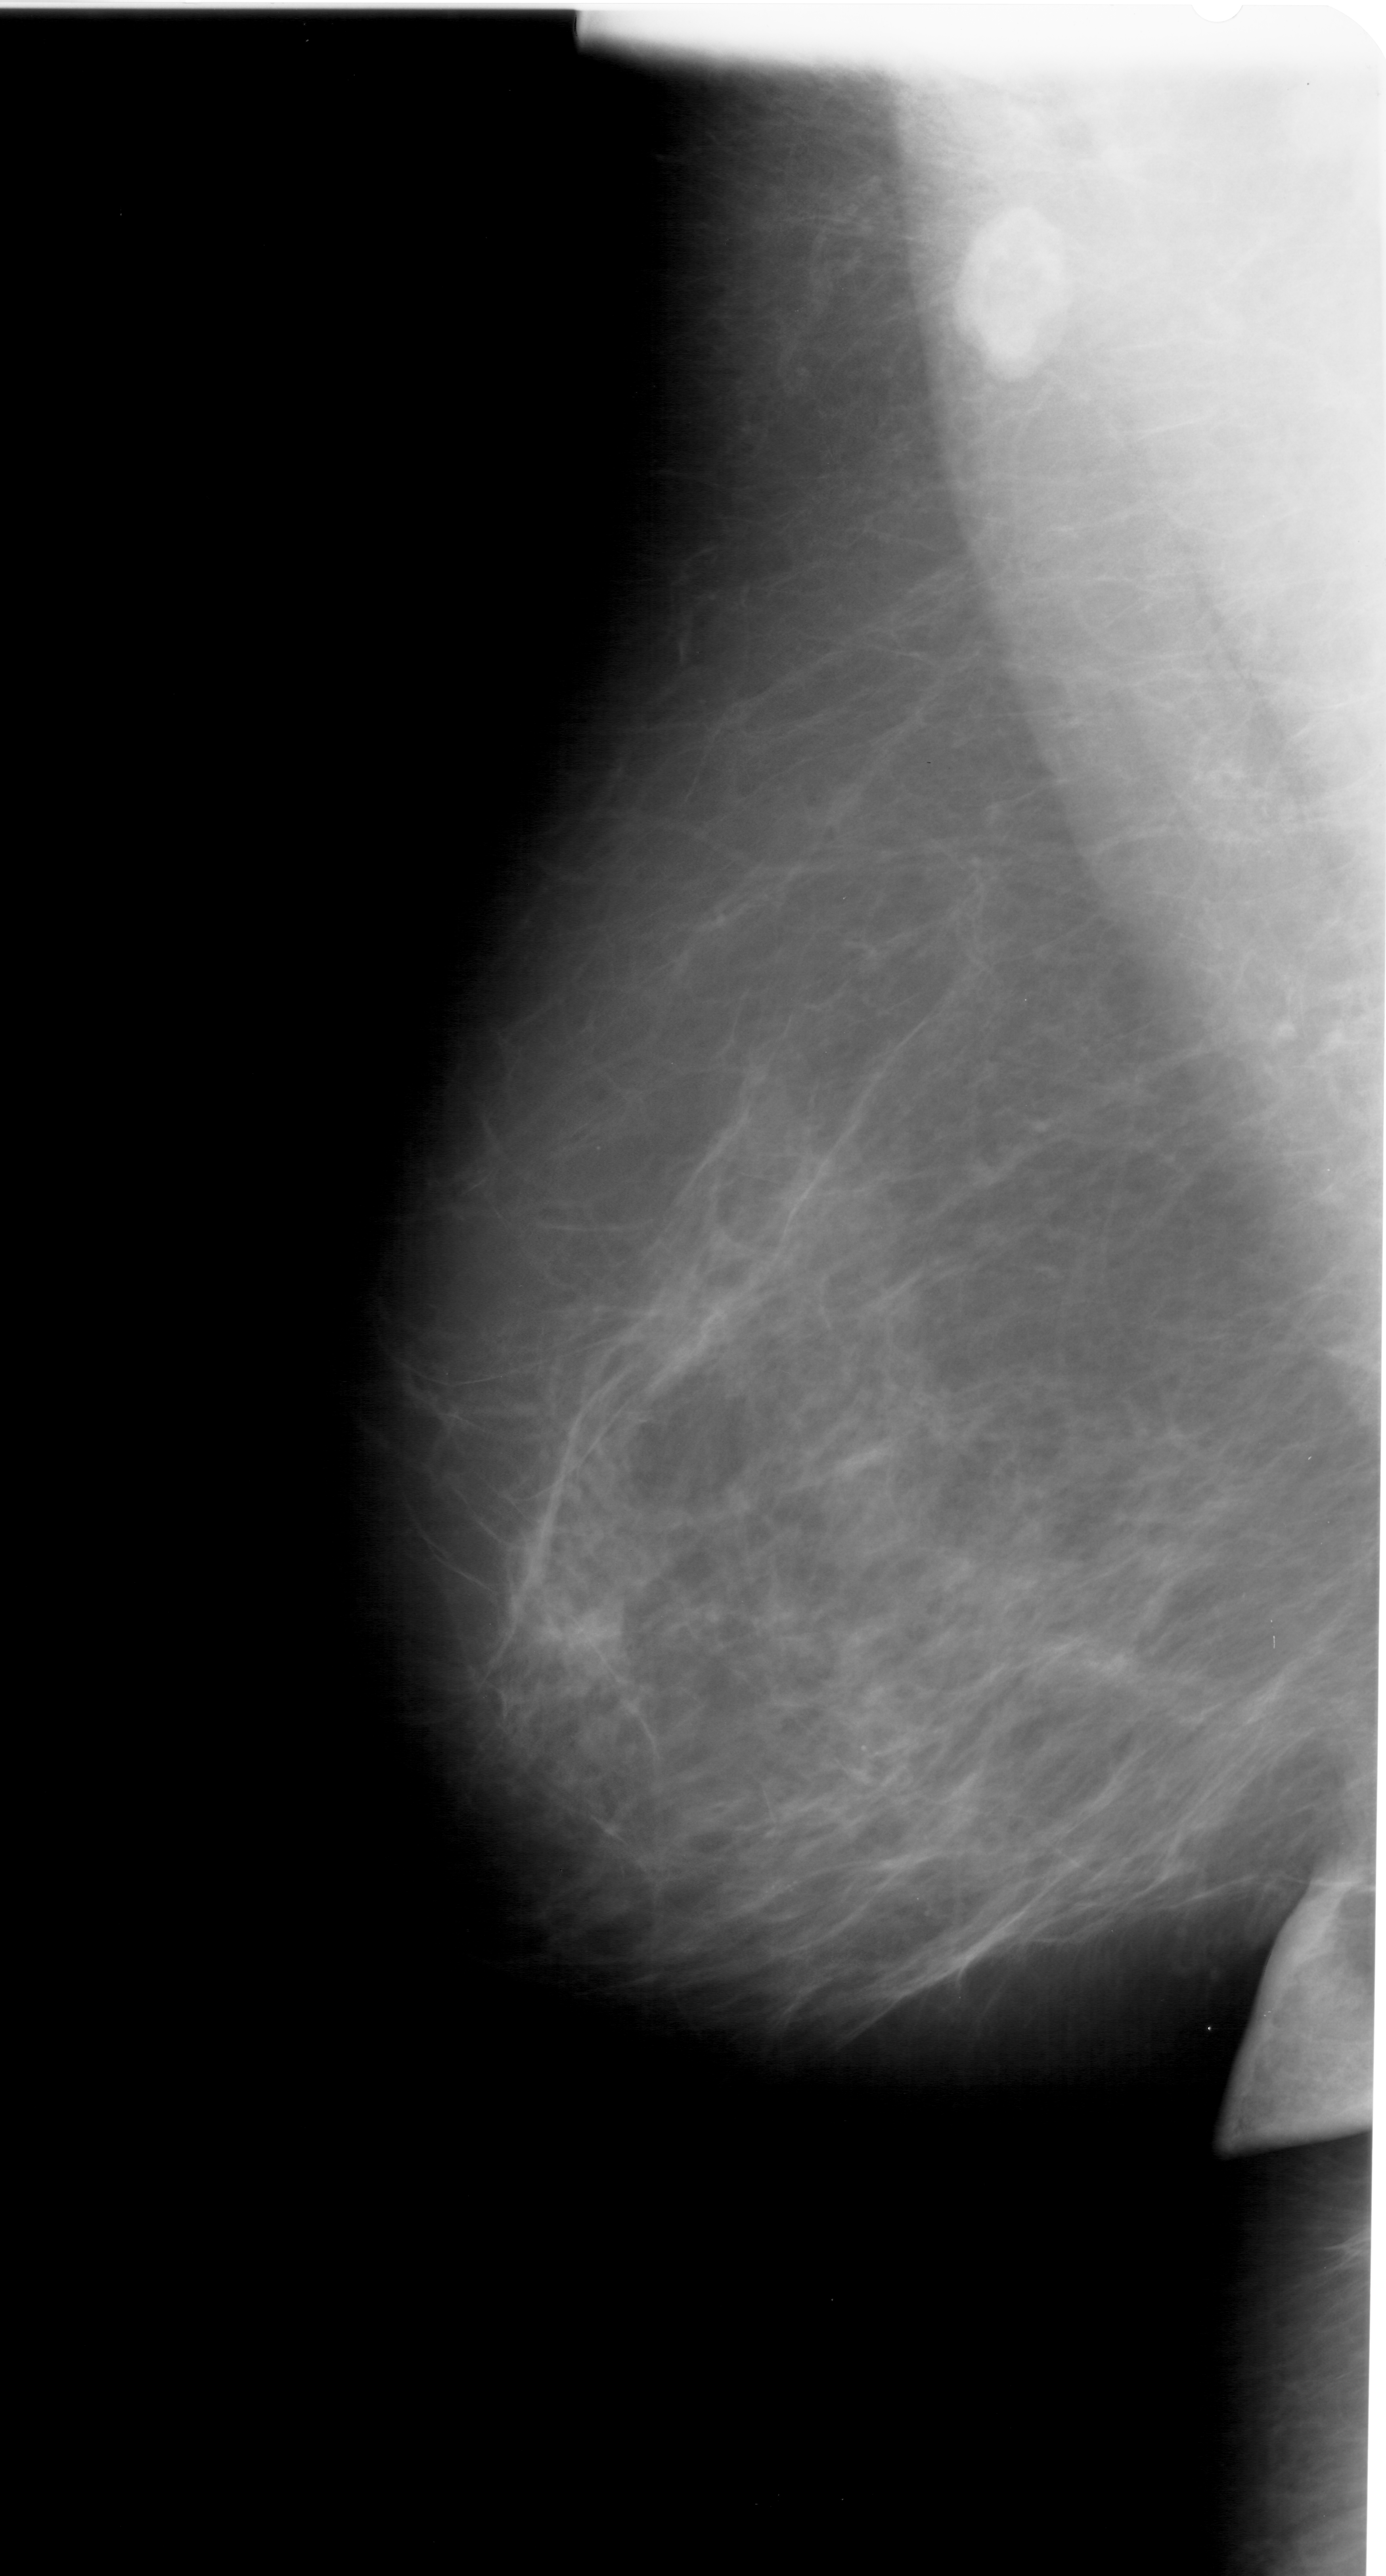
Mammogram (digitized film); left breast; mediolateral oblique (MLO) view; breast composition: scattered fibroglandular densities (BI-RADS density category 2 of 4).
Abnormality record for this image: calcifications, morphology pleomorphic, distribution clustered; BI-RADS assessment category 4; subtlety rating 1 on a 1 (subtle) to 5 (obvious) scale; pathology result (as recorded, not read from the image): benign.